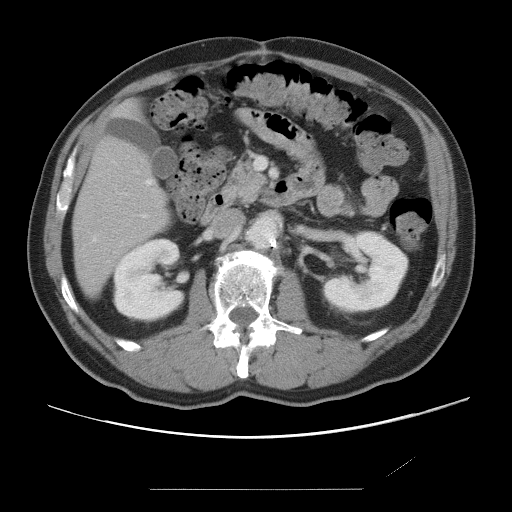
Contrast-enhanced abdominal CT, one axial slice; position 27 of 87 along the scan axis; 120 kVp; soft-tissue window (W 400 / L 40 HU); 5 mm slice thickness; 512 × 512 image matrix, field of view 406 × 406 mm. Male patient, age 74 years. Case-level facts recorded for this patient, not image findings: diagnosis: colorectal cancer liver metastases, imaged before liver resection; multiple liver metastases: yes; largest metastasis: 1.1 cm; chemotherapy before resection: yes.
Outlined on this slice (manually delineated by an expert):
- hepatic veins: box from (x=93, y=180) to (x=152, y=241) px
- liver: (x=73, y=138)–(x=169, y=296)
- planned liver remnant (the part of the liver to remain after resection): (x=73, y=108)–(x=170, y=295)
- portal vein (with intrahepatic branches): (x=143, y=215)–(x=147, y=218)